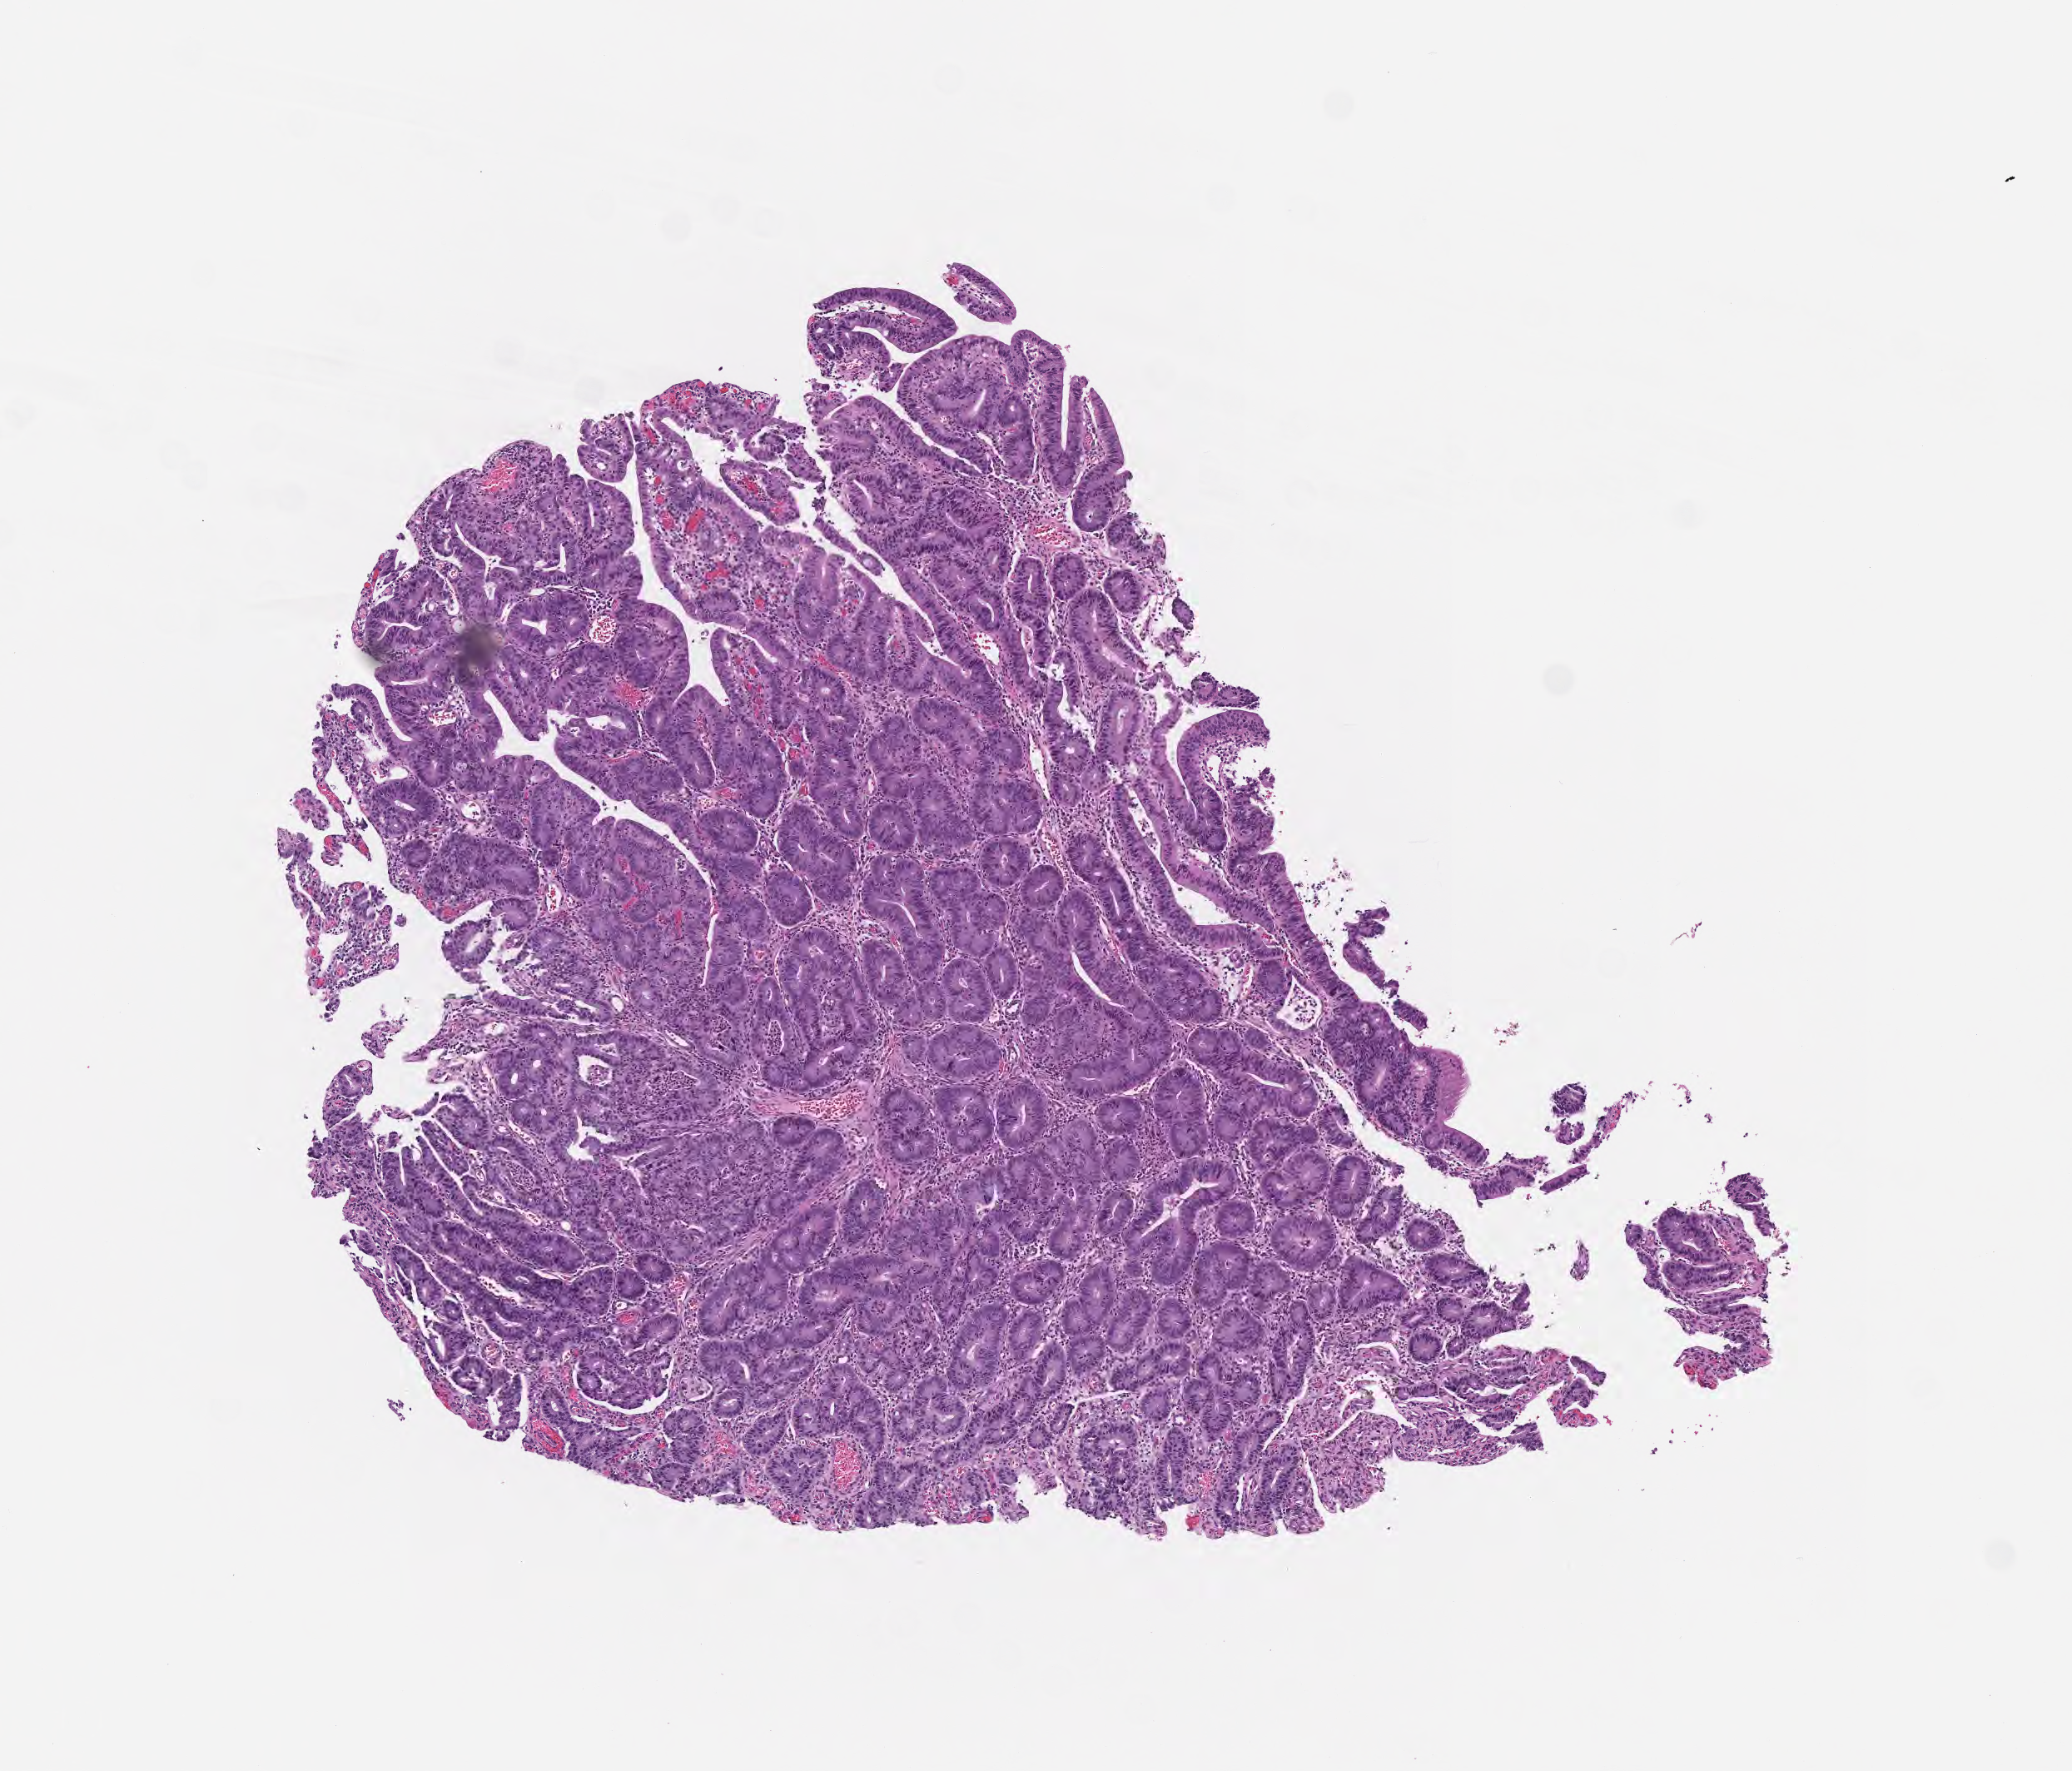
Haematoxylin and eosin whole-slide image — a low-resolution overview of the entire scanned area, about 5.0 x 4.3 mm; FFPE section; primary tumor; site: ileum. Male, age 57 years at initial diagnosis. Tumor grade: G2 (moderately differentiated). Composition of this section per pathologist review: tumor cells 80%, tumor nuclei 80%, stromal cells 20%, necrosis 0%, normal cells 0%. Infiltration values recorded for this section: lymphocyte infiltration 4%, monocyte infiltration 3%, neutrophil infiltration 8%.
• section: bottom of the tissue portion
• AJCC pathologic stage: Stage I
• diagnosis: Adenocarcinoma, NOS